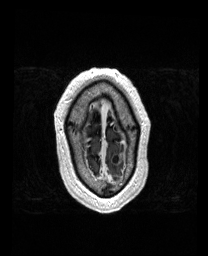
Brain MRI from a brain-tumour surgery series, one axial slice; slice 158 of 192 in the series (ordered by position); T1-weighted post-contrast; 208 × 256 image matrix. From the clinical record (not read from this slice): histopathology: Metastatic Carcinoma from Lung Adenocarcinoma; tumour location: Left Frontal.
Structures marked on this image (outlined manually by an expert reader):
- tumour: box from (x=114, y=157) to (x=121, y=162) px